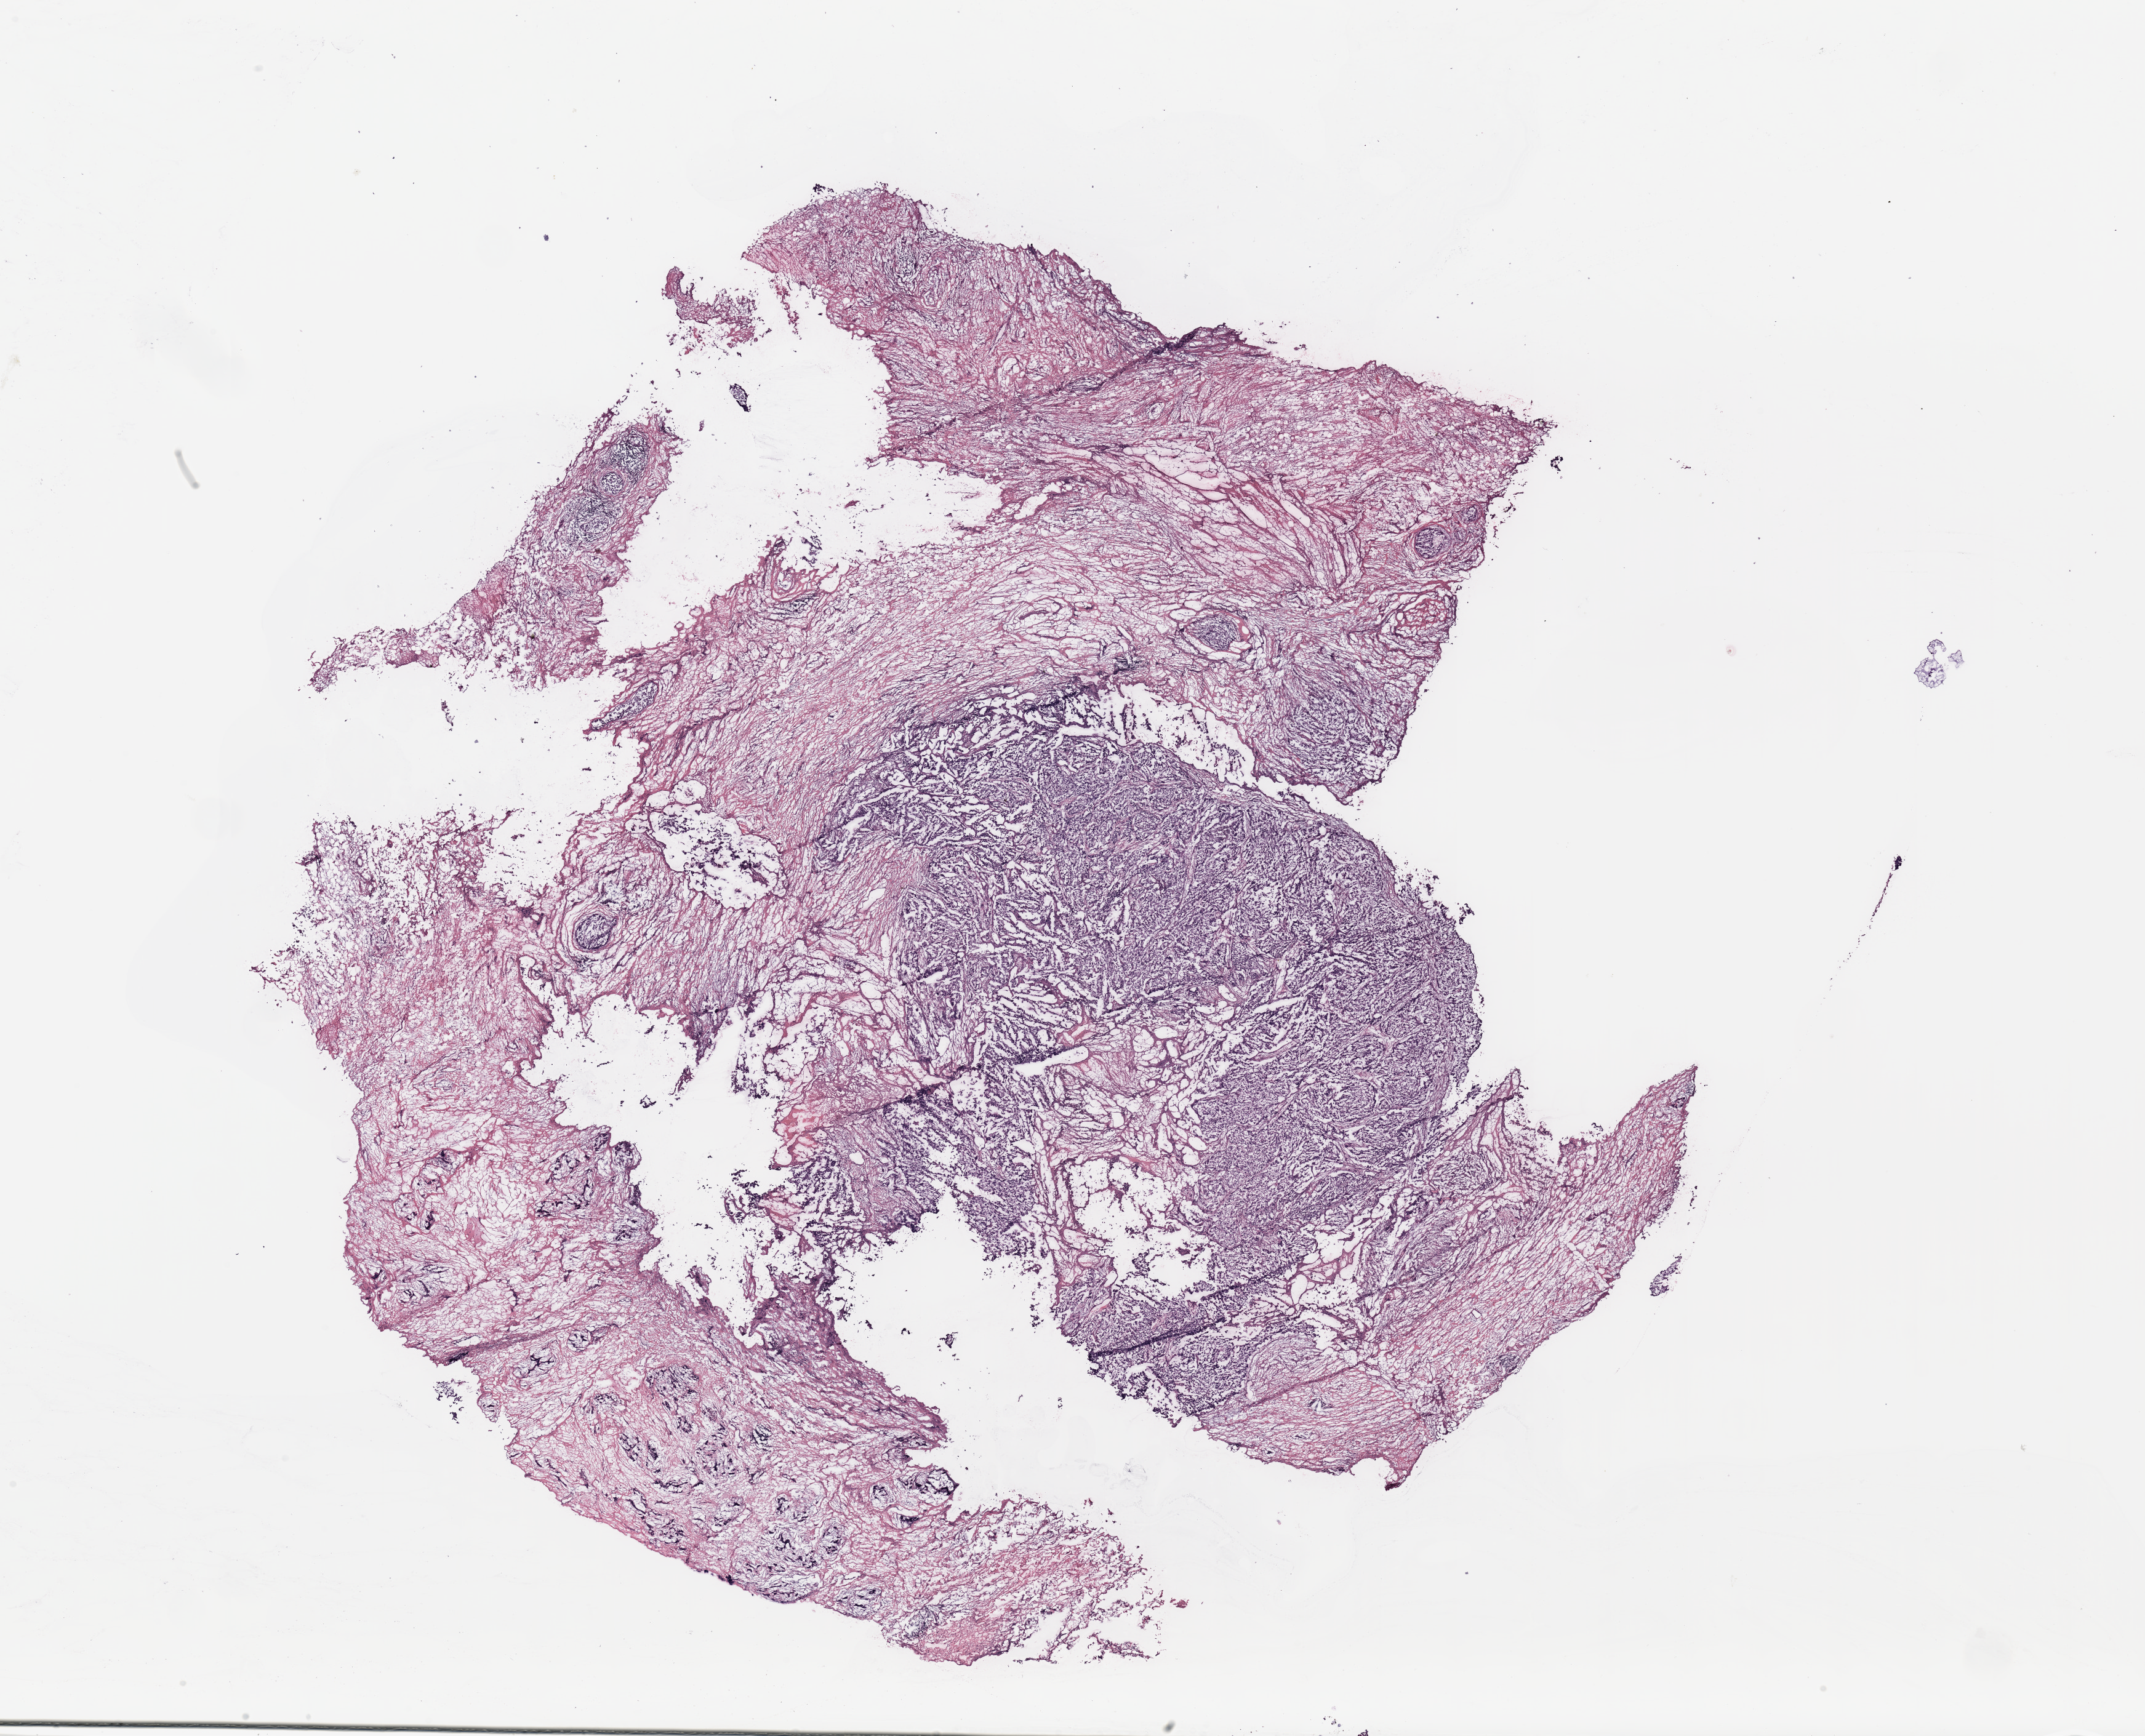
Whole-slide histology image, Hematoxylin and eosin (H&E) stained, low-resolution overview of the scanned area, about 27.6 x 22.3 mm (slide scanned at 20x), breast, tissue type not recorded.
Patient diagnosis (cohort enrolment): breast cancer (breast).